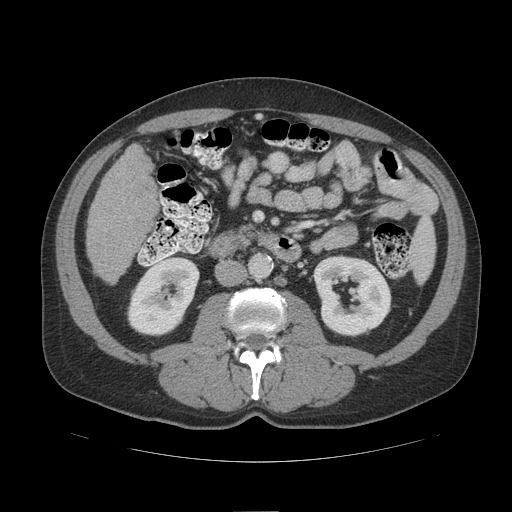
Contrast-enhanced abdominal CT (liver protocol), one axial slice. Position 35 of 109 along the scan axis. Reconstruction kernel STANDARD. 140 kVp. Soft-tissue window (W 400 / L 40 HU). 2.5 mm slice thickness. 512 × 512 image matrix, field of view 420 × 420 mm. From the clinical record (not read from this slice): diagnosis: hepatocellular carcinoma (patient treated with transarterial chemoembolisation; whether this scan precedes or follows treatment is not stated here); TNM stage (as recorded): Stage-IIIB; Child-Pugh class: A.
Outlined on this slice (semi-automatic segmentation, software-assisted and operator-edited):
- liver parenchyma outside the tumour (the mass and vessels are separate outlines, so this box may not span the whole liver): box from (x=86, y=144) to (x=157, y=282) px